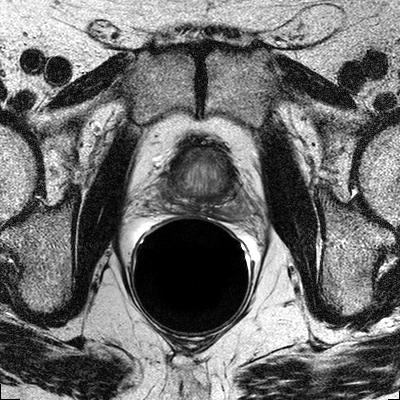
Multiparametric prostate MRI examination; 3 images, each a single mid-volume slice chosen by position (not for content). Treatment context recorded for this patient: No surgery, was considered for radiation theraphy.
Image 1: T2-weighted axial slice, series "T2W_TSE_AX", slice 17 of 32, 3 mm slice thickness.
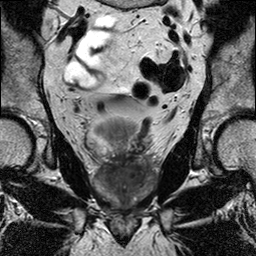
Image 2: coronal T2-weighted image, slice 13 of 24.
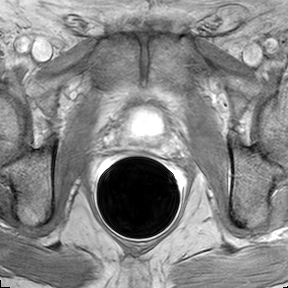
Image 3: axial dynamic contrast-enhanced (DCE) T1-weighted image, series "AX BLISS_GAD_8", slice 17 of 32, dynamic phase 5 of 8, 6 mm slice thickness.
MRI report (verbatim):
The prostate has a maximal lateral diameter of 4.7cm, a maximal craniocaudal diameter of 3.9cm and a maximal AP diameter of 2.7 cm resulting in an estimated gland volume of 26 cc. The zonal anatomy is preserved. The entire prostate shows on the T2-weighted images a diffuse fine linear and fine nodular hypointense signal alterations compatible with chronic prostatitis. Smallest foci (smaller than 4 mm) of cancer cannot be excluded. On the dynamic contrast-enhanced series there is a 1.7 x 0.7 cm area of suspicious wash-in and washout seen in the left peripheral zone between 9 and 6:00 in the prostate base and midthird. No evidence for involvement of the neurovascular bundle on either side. No evidence for seminal vesicles infiltration. No evidence of involvement of bladder neck and rectal wall. No suspiciously enlarged obturator and iliac lymph nodes. IMPRESSION: 1) 1.7 cm area of highly suspicious enhancement in the left posterior lateral (between 9-6 o clock) peripheral zone of the midthird and base of the prostate. 2) On the background of diffuse chronic prostatitis. Small foci of cancer on the right cannot be excluded (smaller than 4 mm). 3) No evidence of extraprostatic disease on either side. Unremarkable Seminal vesicles 4) No pelvic lymphadenopathy.

Biopsy pathology report for this patient (as recorded):
Gross Description The specimen consists of multiple core fragments of tan soft tissue measuring 0.5cm to 2.3cm in length and 0.1cm in diameter. The specimen is submitted in six cassettes.1-right pz, 2-right pz/tz, 3-right apex, 4-left pz, 5-left pz/tz, 6-left apex. 1. RIGHT PZ: PROSTATIC ADENOCARCINOMA, GLEASON SCORE 3+4=7/10, INVOLVING TWO CORES, ABOUT 20% OF TISSUE REPRESENTED. 2. RIGHT PZ/TZ: BENIGN PROSTATIC TISSUE, NO TUMOR IDENTIFIED. 3. RIGHT APEX: BENIGN PROSTATIC TISSUE, NO TUMOR IDENTIFIED. 4. LEFT PZ: PROSTATIC ADENOCARCINOMA, GLEASON SCORE 3+4=7/10, INVOLVING TWO CORES, ABOUT 30% OF TISSUE REPRESENTED. 5. LEFT PZ/TZ: BENIGN PROSTATIC TISSUE, NO TUMOR IDENTIFIED. 6. LEFT APEX: BENIGN PROSTATIC TISSUE, NO TUMOR IDENTIFIED.